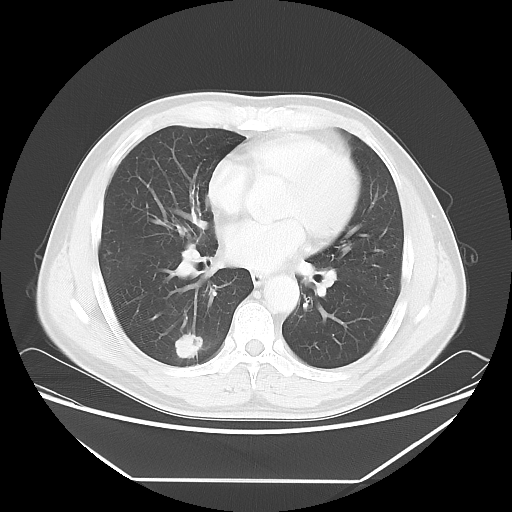
Chest CT, one axial slice. Position 31 of 65 along the scan axis. Reconstruction kernel LUNG. Lung window (W 1500 / L -600 HU). 512 × 512 image matrix. Patient: male, 50 years. From the clinical record (not read from this slice): clinical TNM (as recorded): T1c N0 M0.
Structures marked on this image (rectangle marked by the reading radiologist):
- lung tumour (recorded histology: adenocarcinoma): bounding box [x1, y1, x2, y2] px = [173, 332, 205, 364]